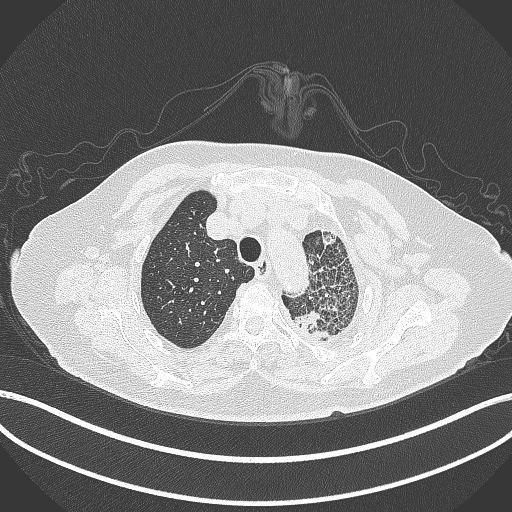
Chest CT, one axial slice. Position 321 of 399 along the scan axis. 120 kVp. Lung window (W 1500 / L -600 HU). 1 mm slice thickness. 512 × 512 image matrix, field of view 400 × 400 mm. Female patient, age 75 years. Case-level facts recorded for this patient, not image findings: clinical TNM (as recorded): T3 N3 M1.
Structures marked on this image (bounding box drawn by a radiologist):
- lung tumour (recorded histology: adenocarcinoma): bounding box (x1, y1, x2, y2) in pixels: (293, 307, 339, 350)